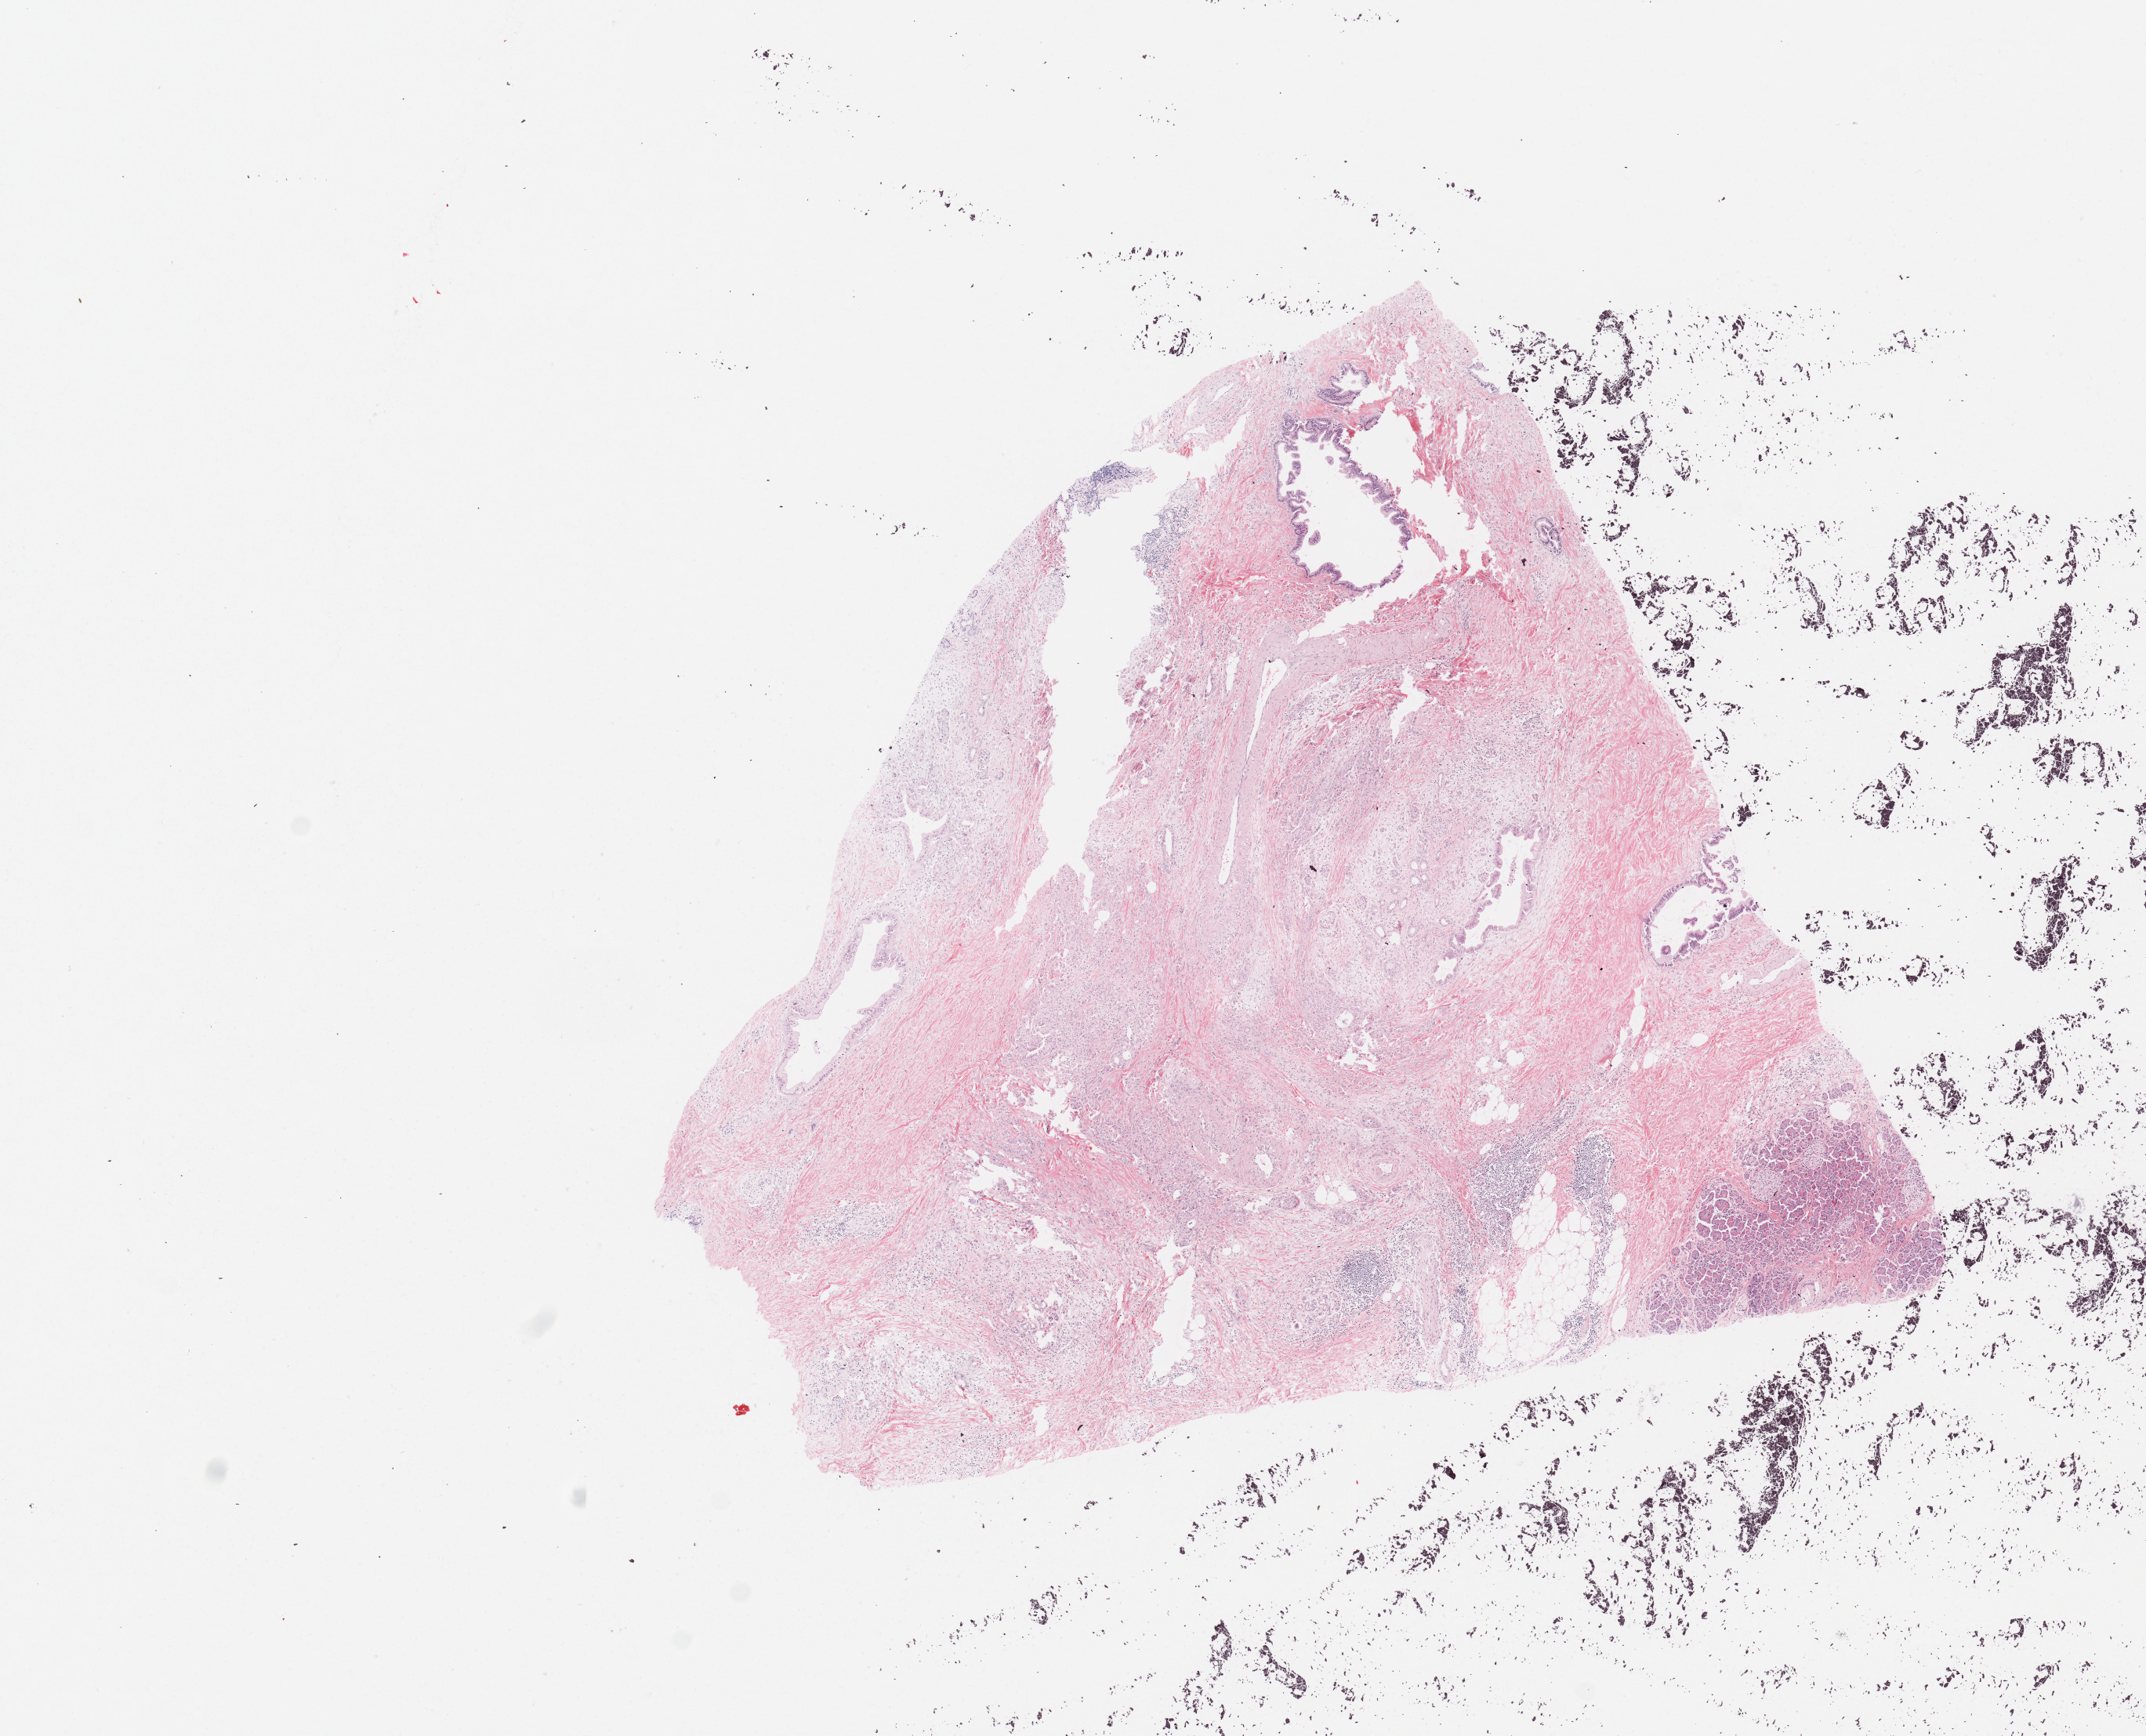
Digitized H&E-stained tissue section (whole slide) — low-resolution overview of the scanned area, about 10.8 x 8.8 mm (slide scanned at 20x), tumour tissue sample, pancreas. 67-year-old female patient.
- patient diagnosis (cohort enrolment): ductal adenocarcinoma (pancreas)
- primary tumour site (as recorded): head